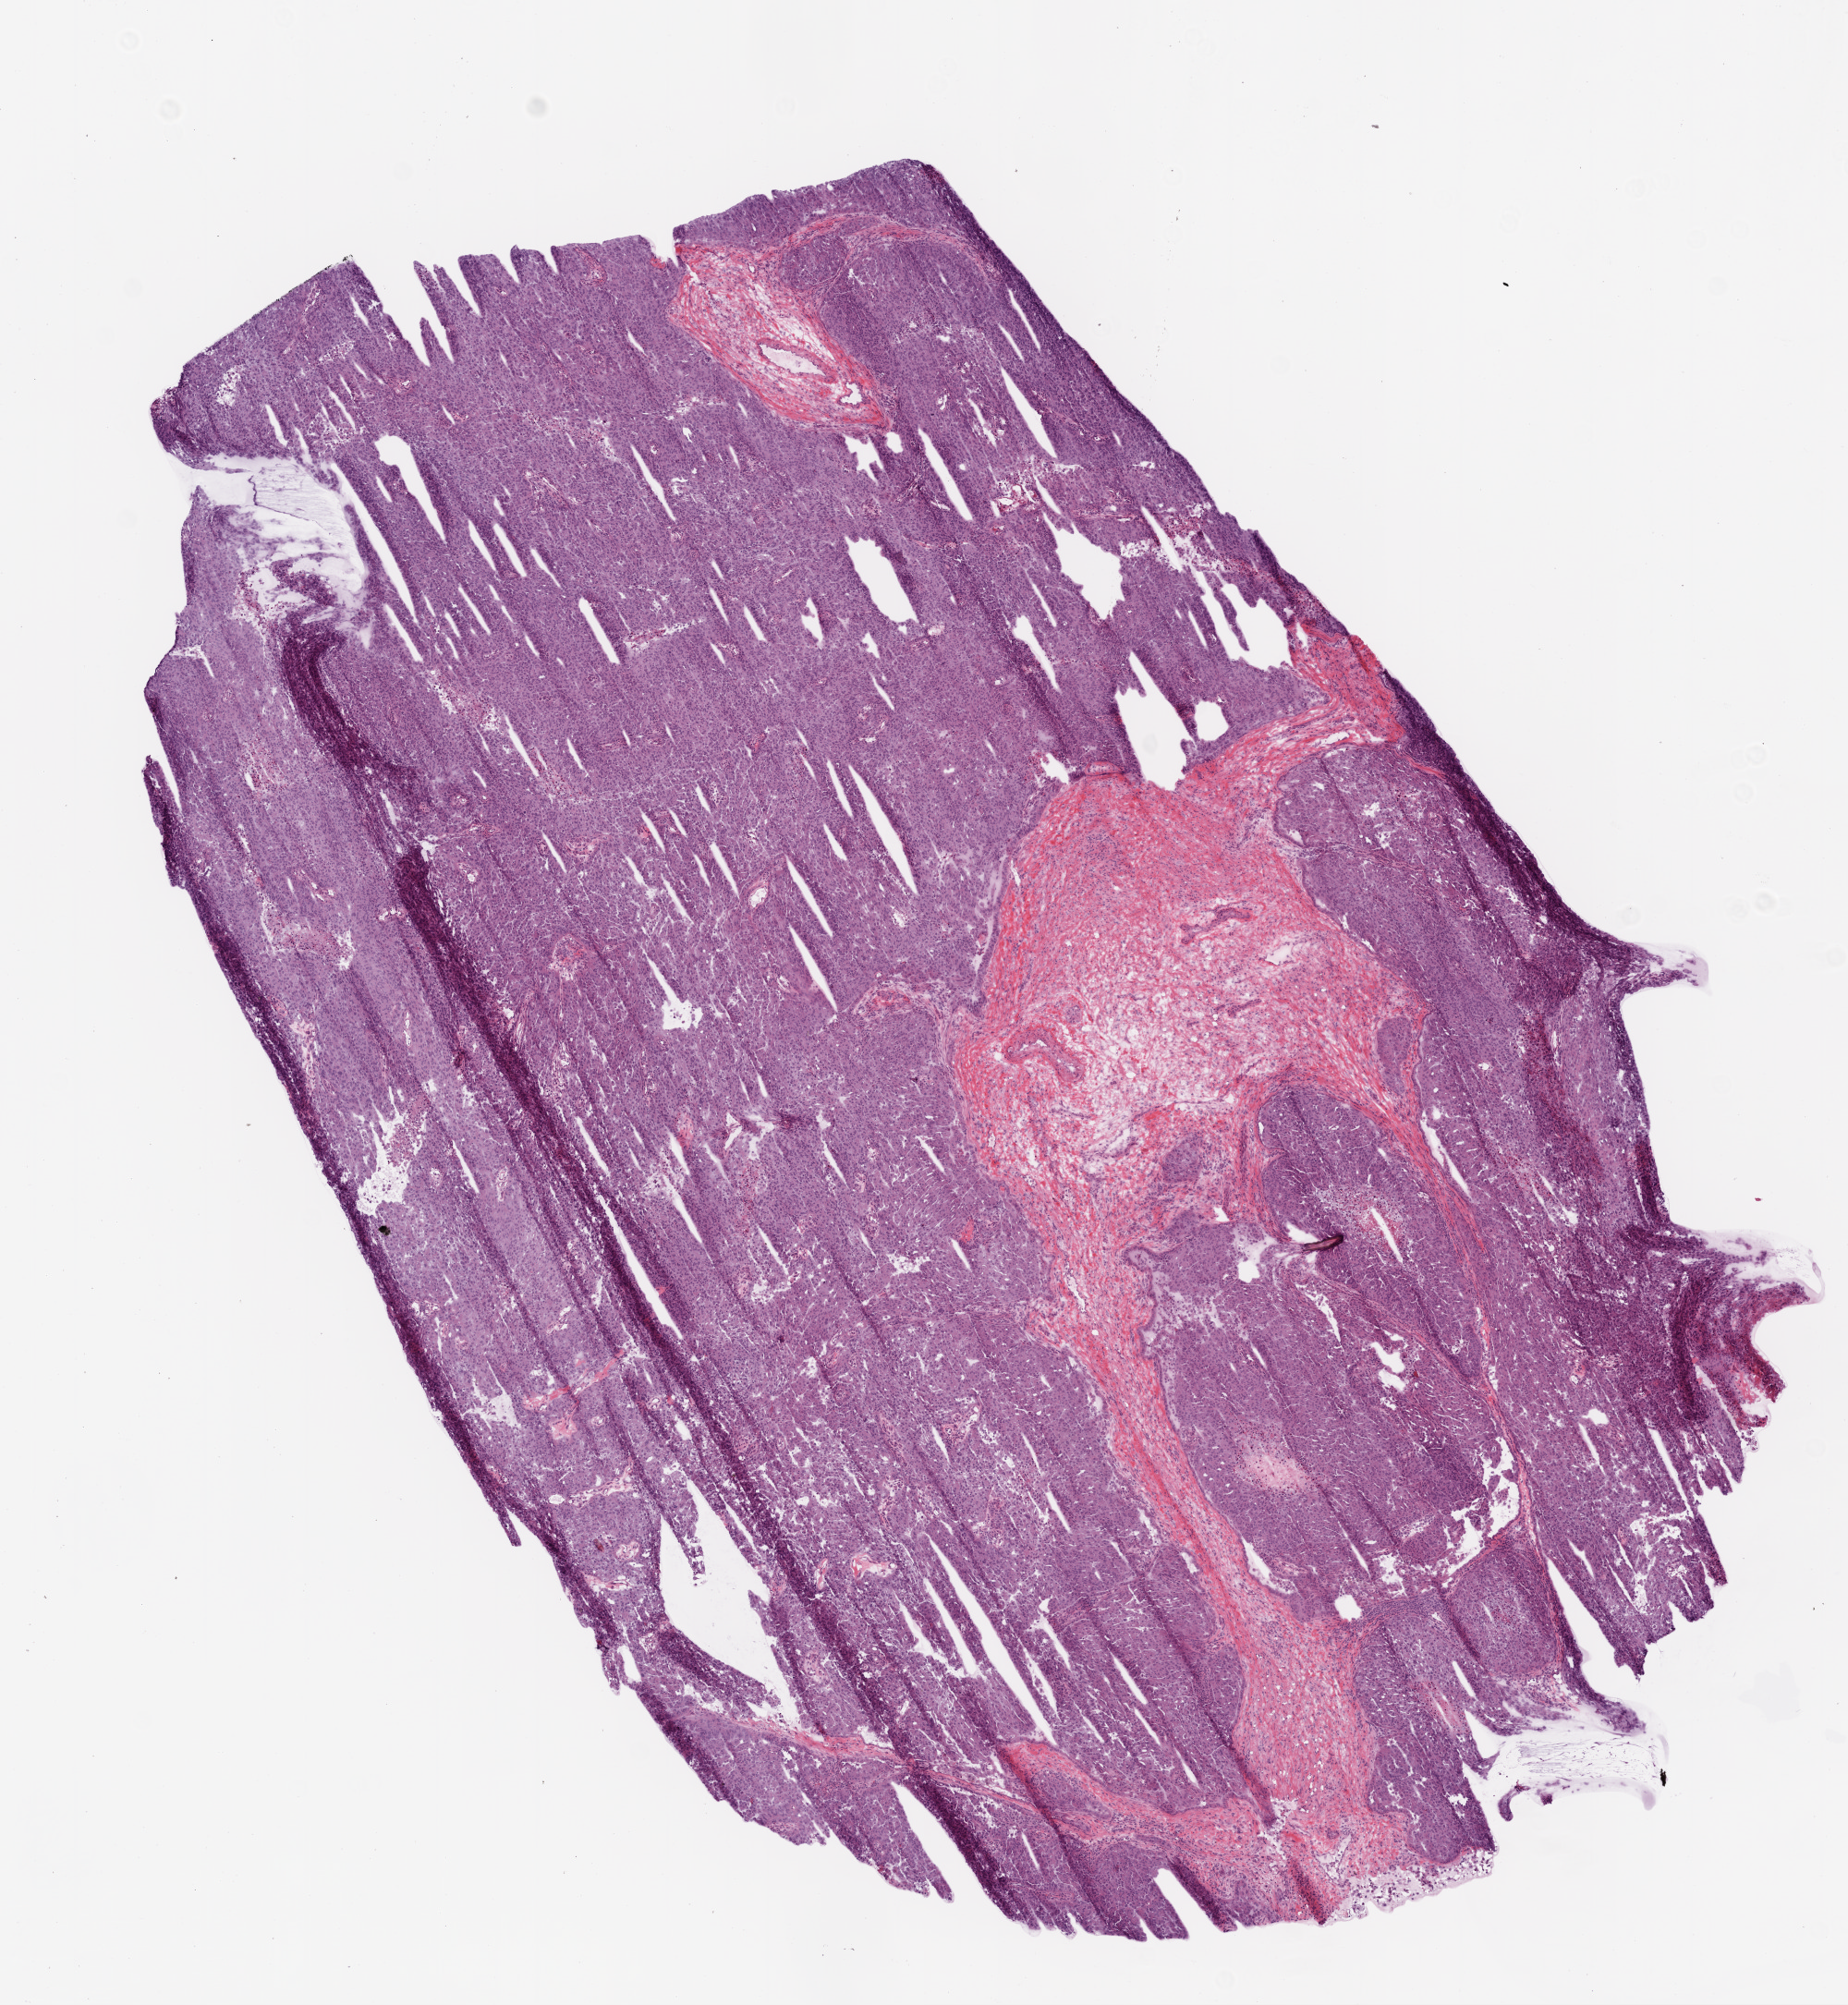
Digitized H&E tissue section (whole slide) — shown as a low-resolution overview of the whole scanned area (about 8.0 x 8.7 mm, acquisition: 20x scan). Frozen section from the bottom of the tissue portion. Ovary, primary tumour sample. Female patient; age at initial diagnosis 63 years. Histologic grade: G3 (poorly differentiated). Composition of this section per pathologist review: tumour cells 90%, tumour nuclei 95%, normal cells 0%, stromal cells 8%, necrosis 2%.
Diagnosis: Serous cystadenocarcinoma, NOS. FIGO stage: IV.